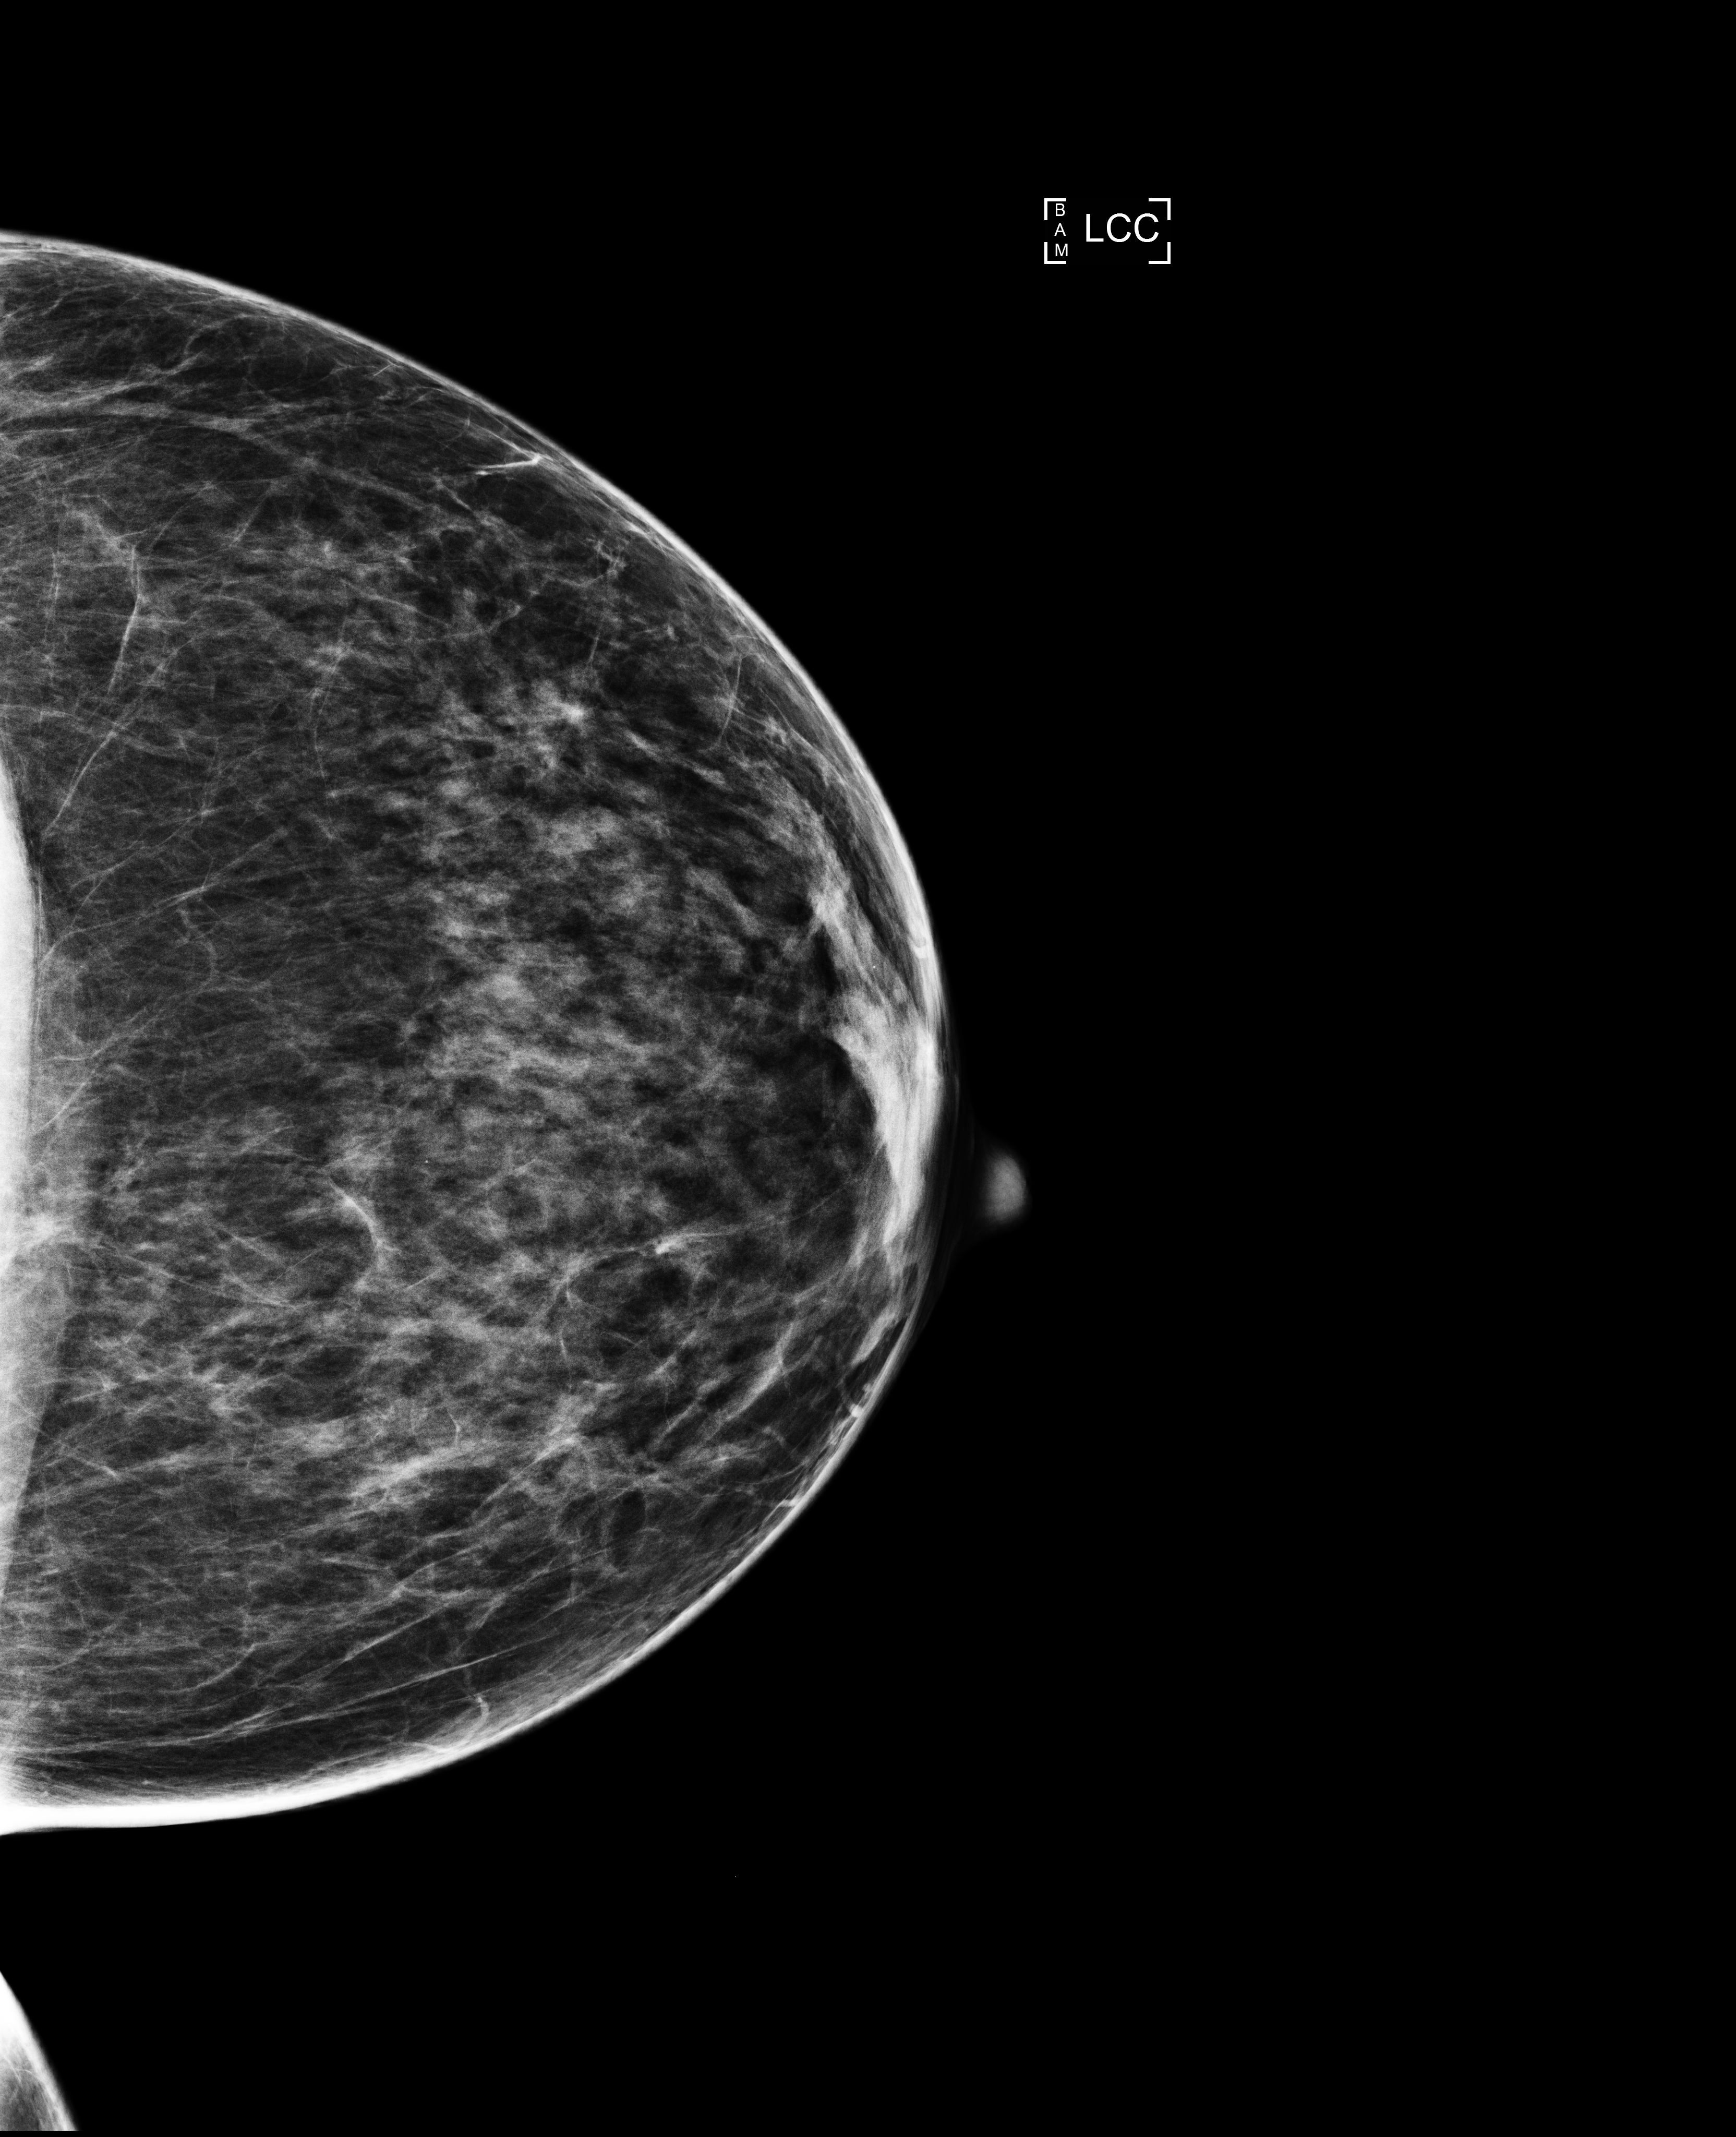
Screening examination, compressed breast thickness 63 mm. Female patient, age 44 years.
Image type: full-field digital mammogram. Breast: left. Projection: CC view.